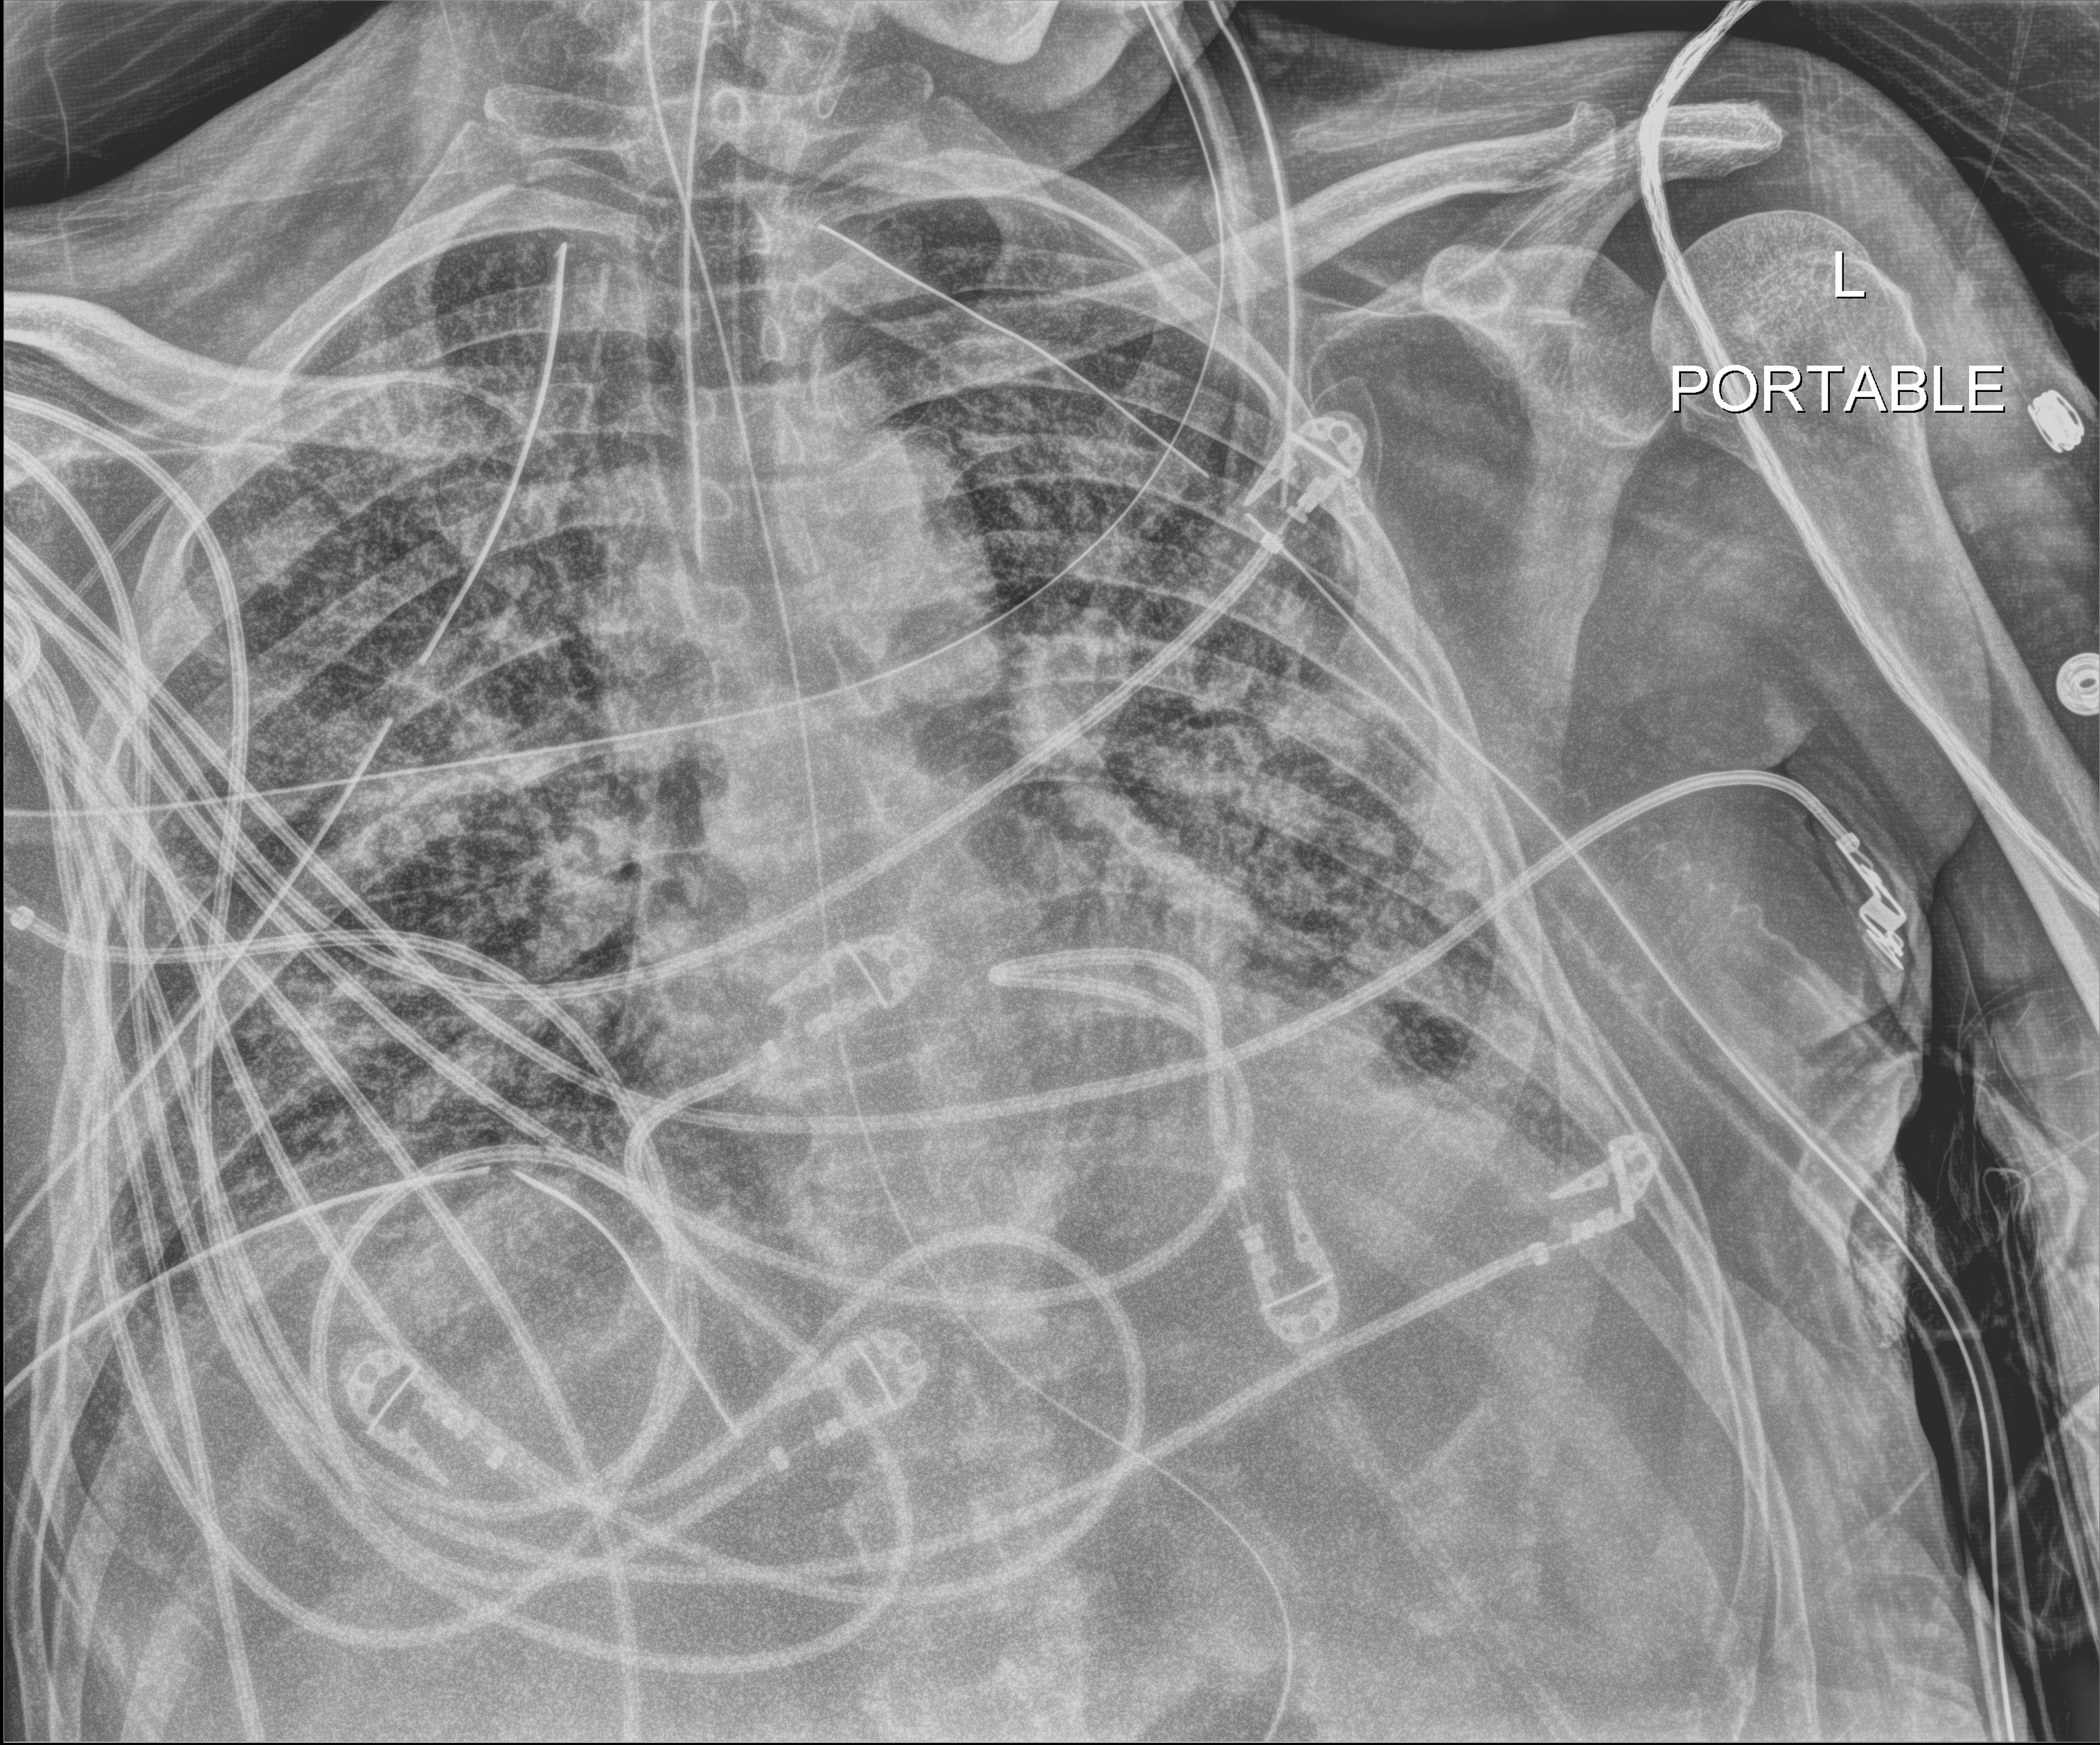
Portable chest radiograph. Patient hospitalised with COVID-19; male, aged 18–59 years.
Admission-level facts for this patient (not findings on this image; timing relative to this image not recorded): chronic kidney disease (admission record): no.